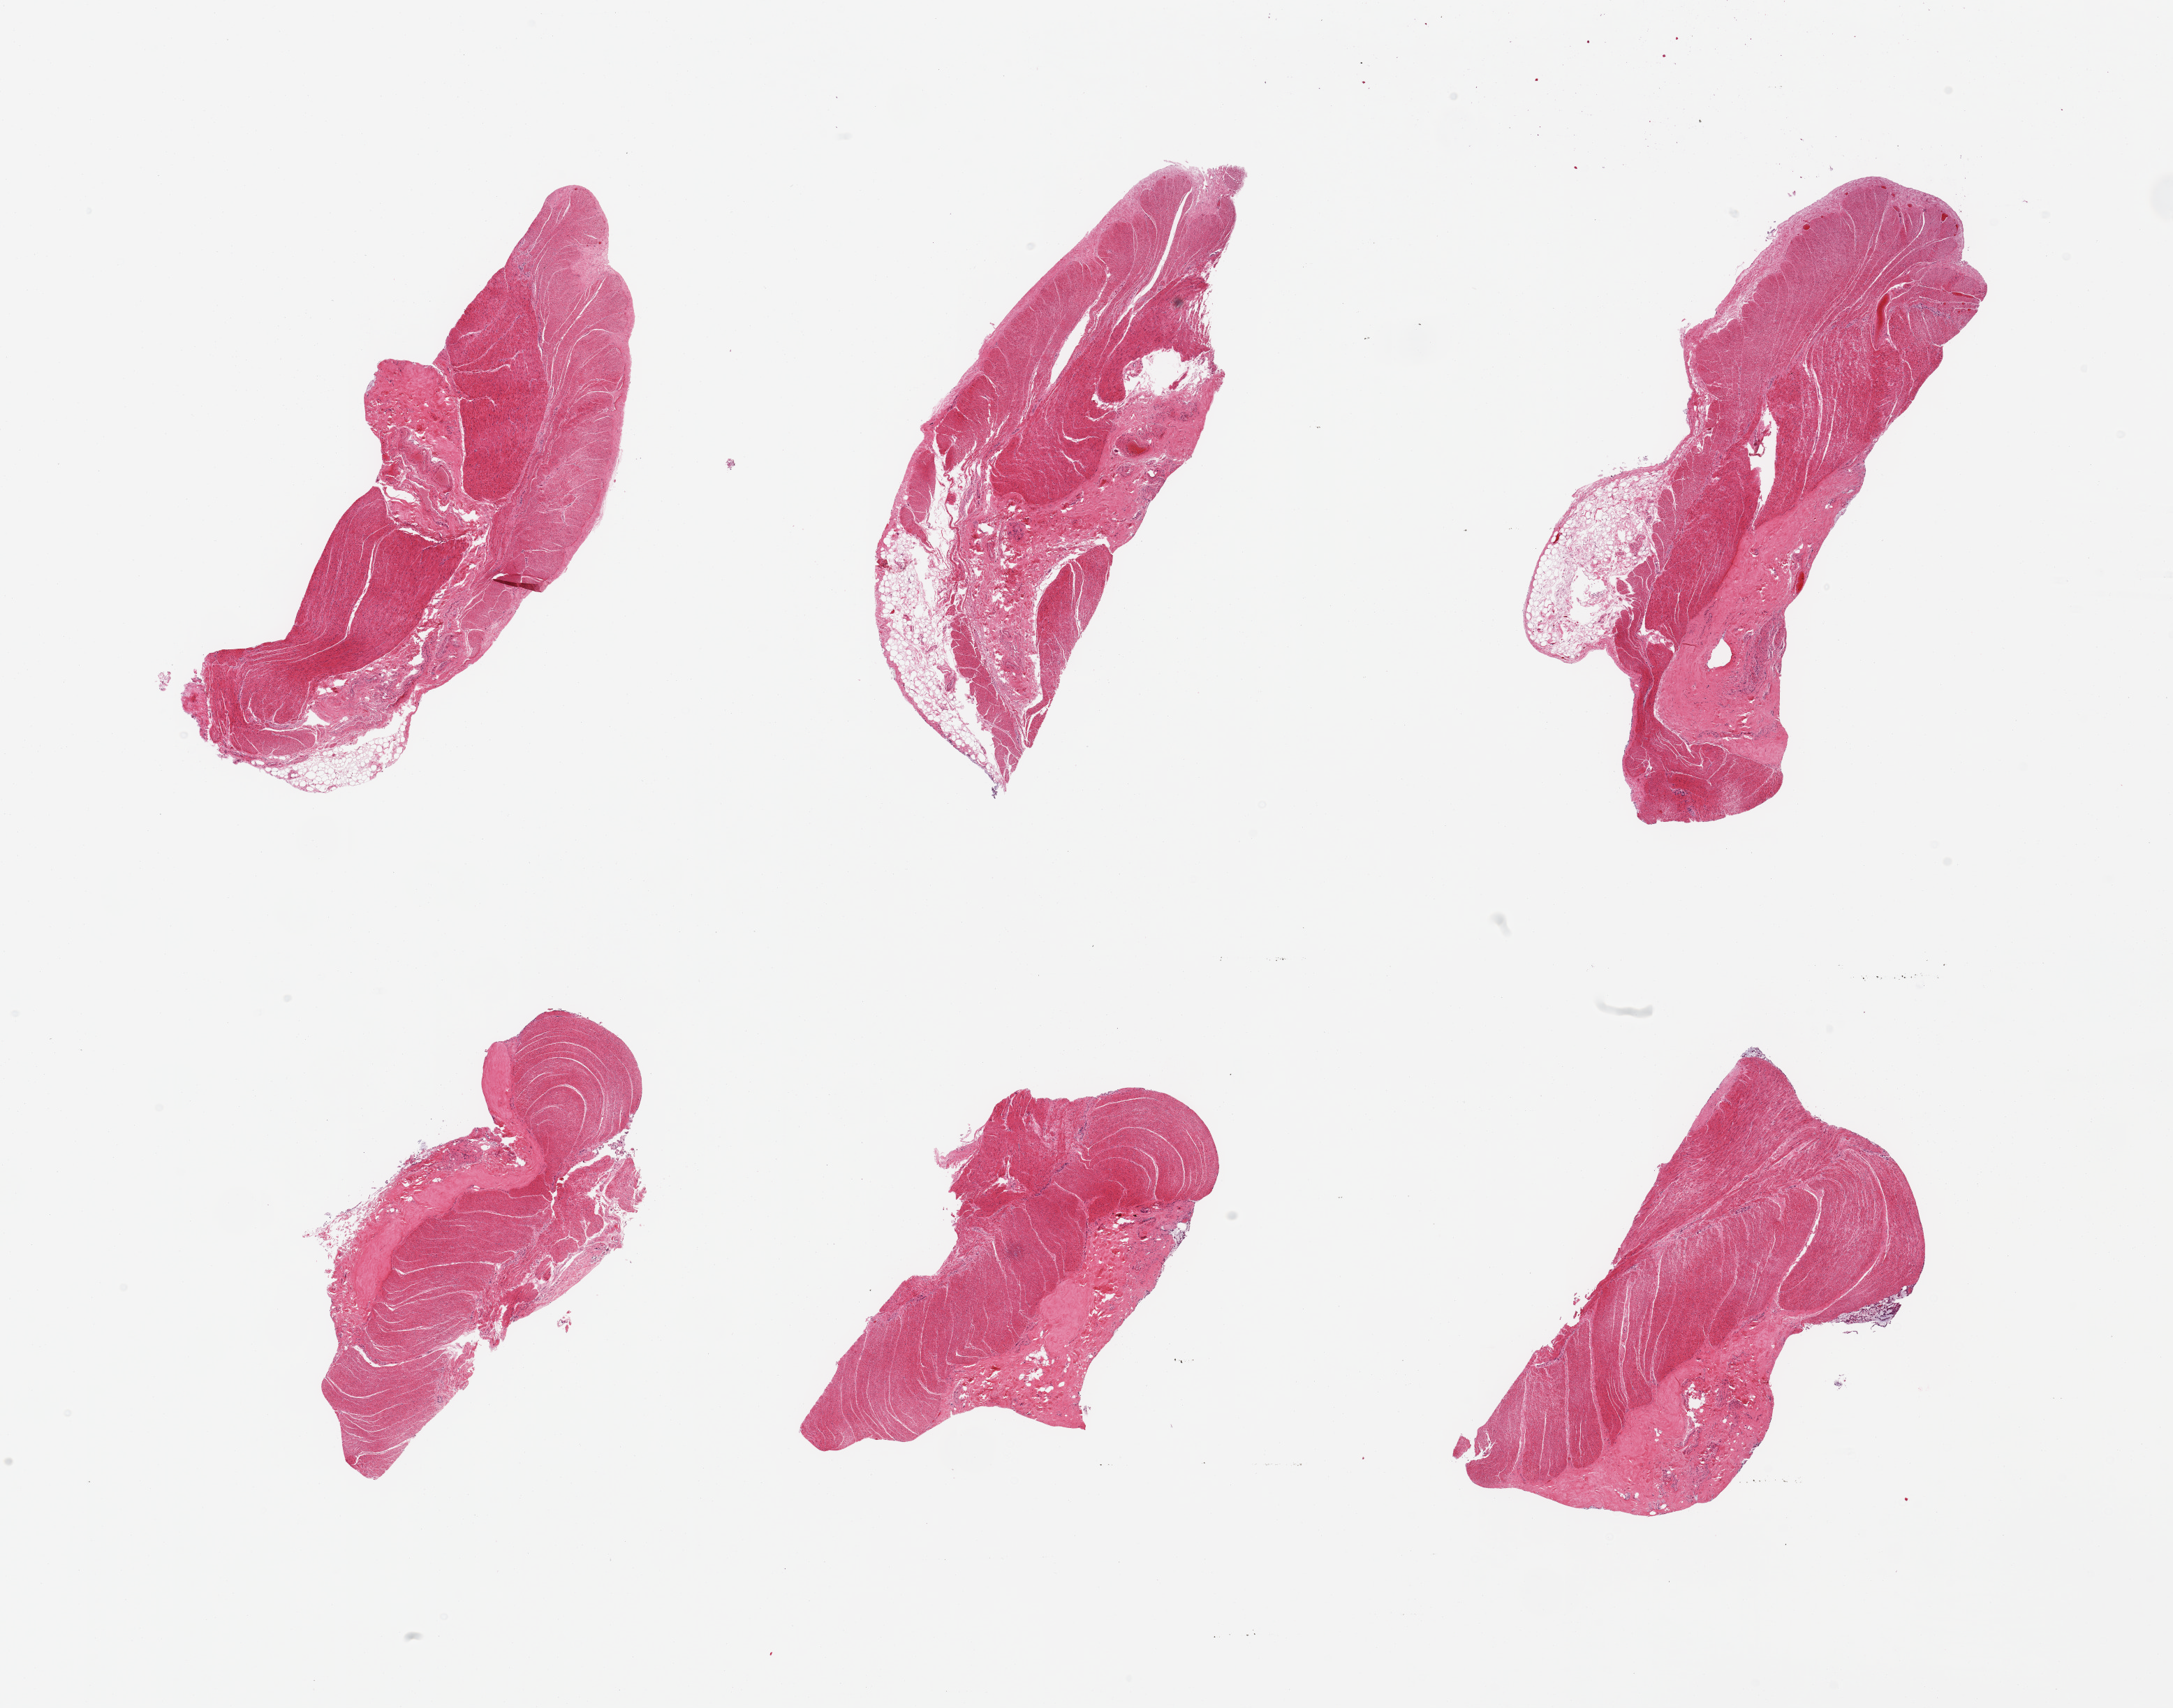
Haematoxylin and eosin whole-slide image, shown as a low-resolution overview of the whole scanned area (about 24.6 x 19.3 mm, slide scanned at 20x), PAXgene-fixed paraffin-embedded (PFPE) section, target tissue: sigmoid colon, tissue donor sample. Donor sex: female.
Reviewer comment on this tissue sample: 6 pieces, confirmed target muscularis; adherent nubbins of fat up to ~1mm.